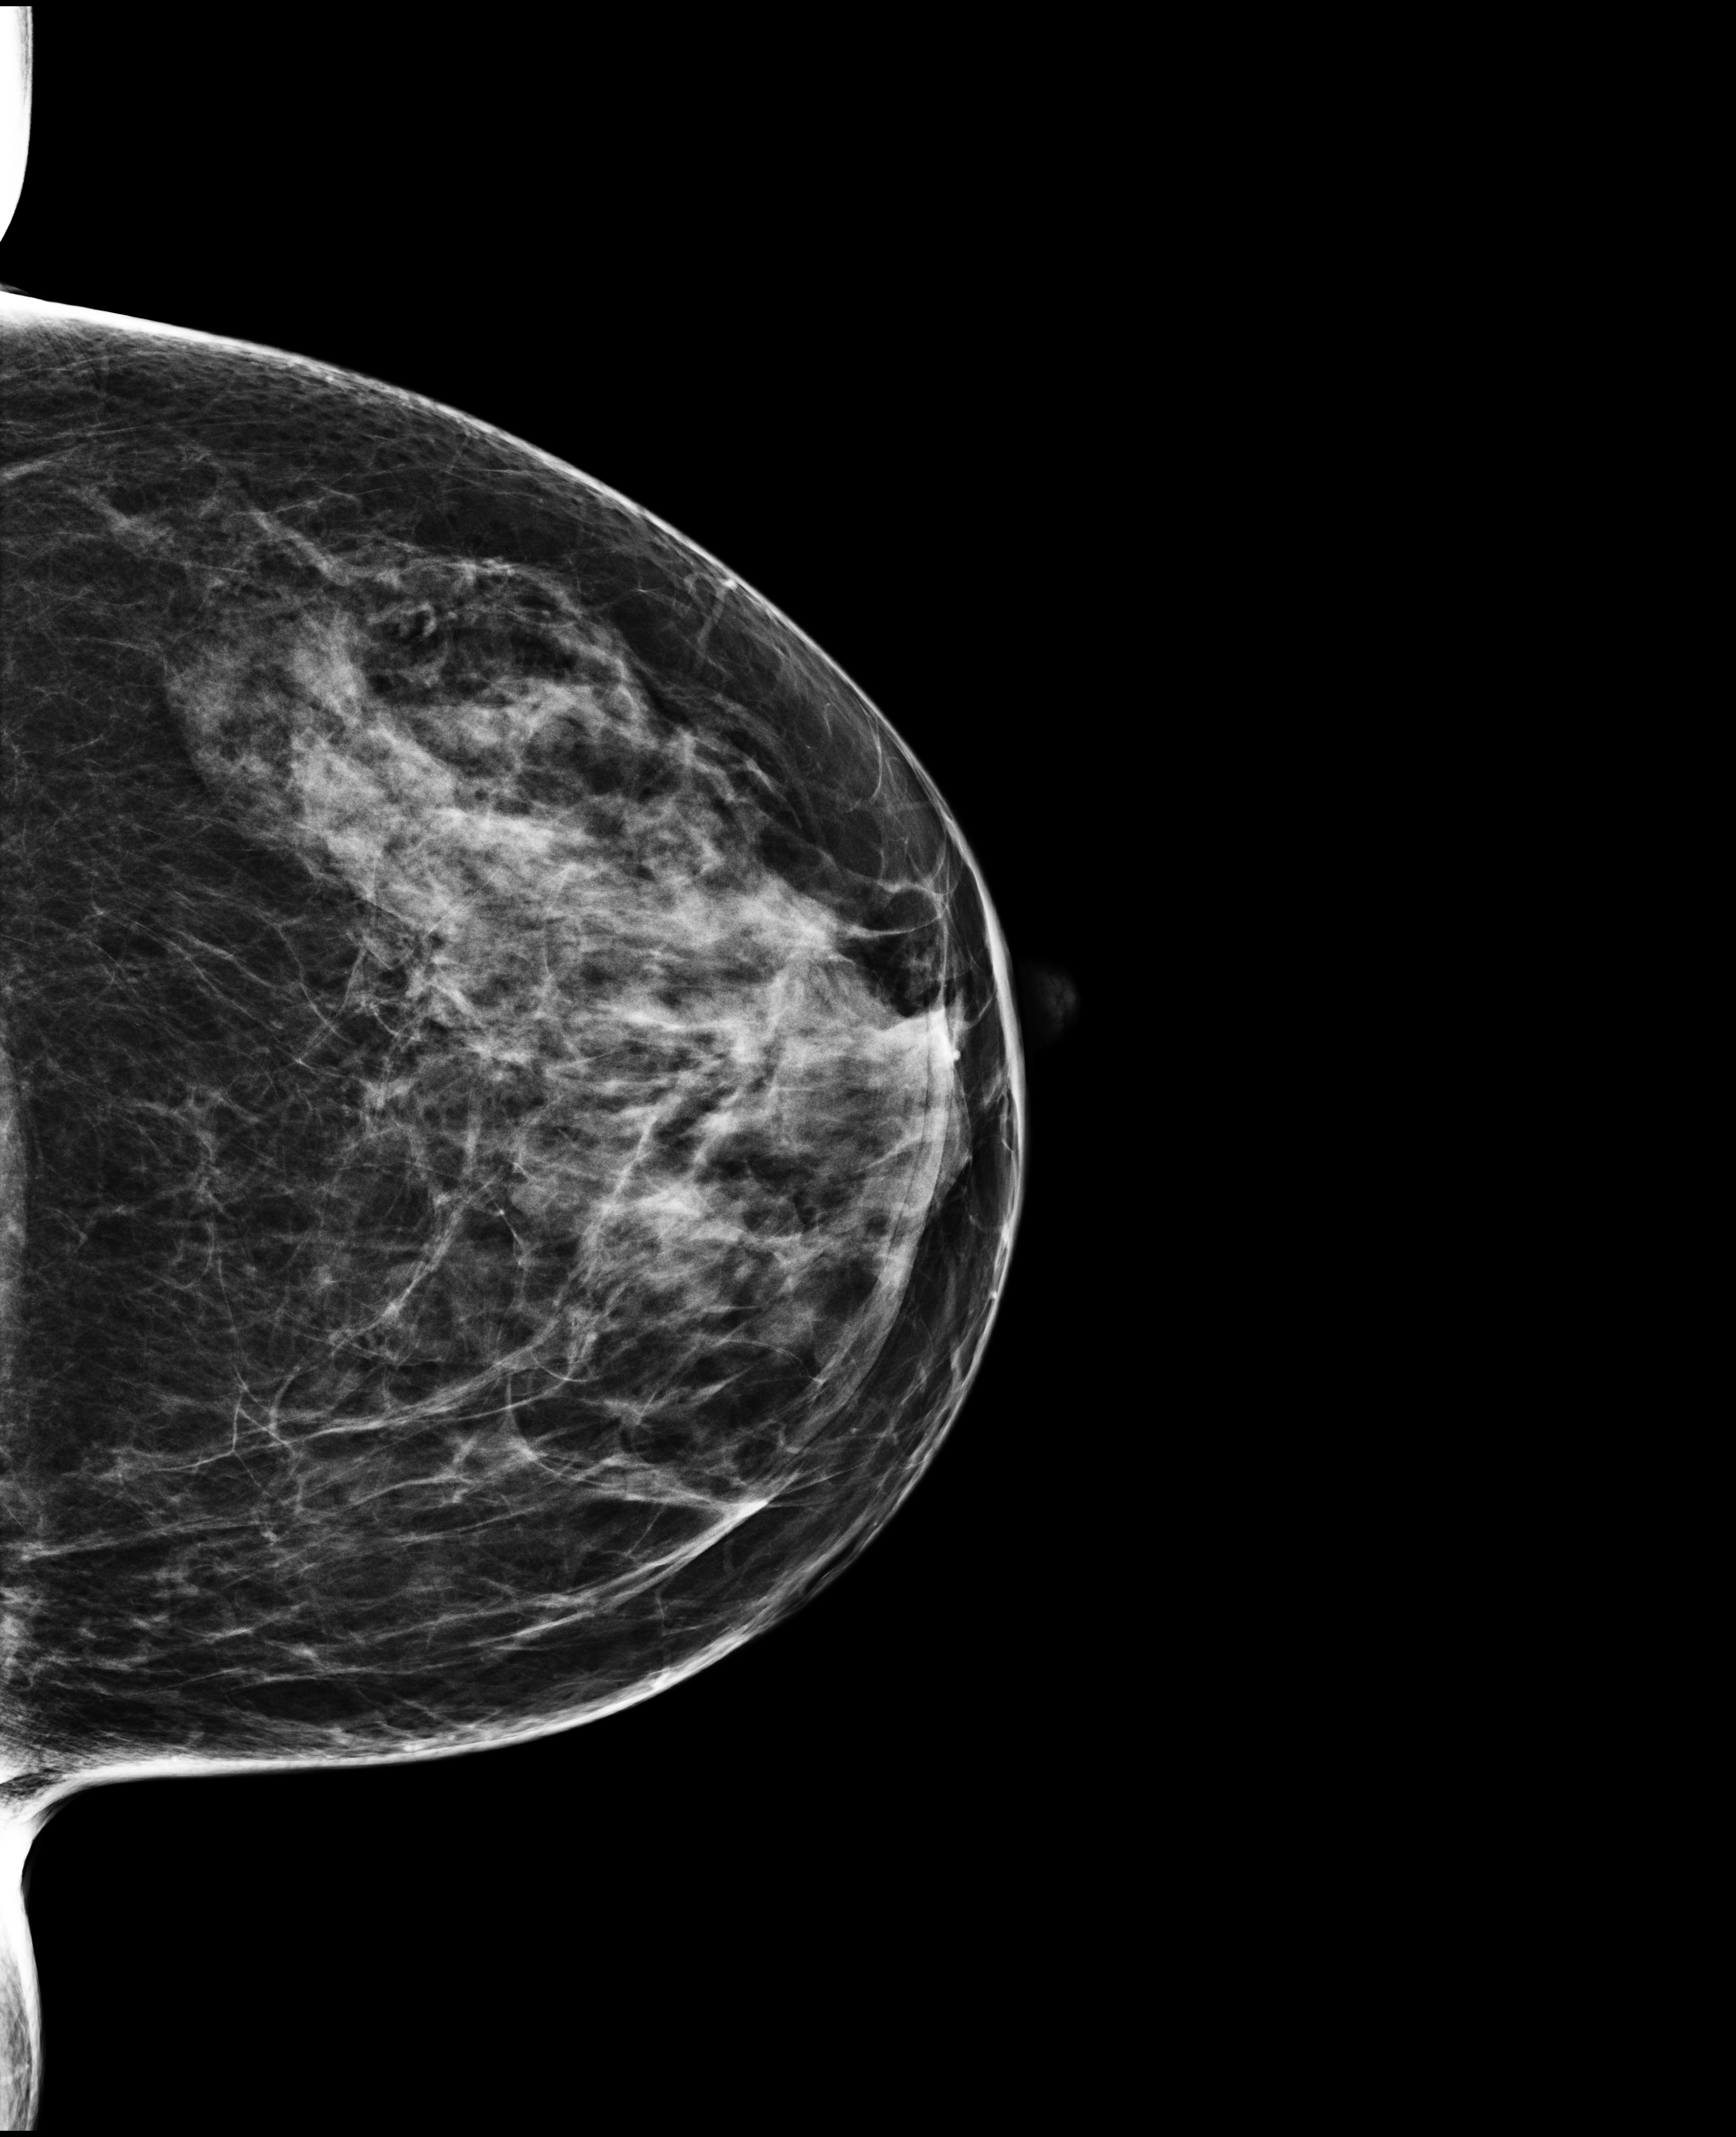
Screening examination. Patient aged 53 years (female).
Image type: full-field digital mammogram. Breast: left. Projection: craniocaudal (CC) view. Breast density at the screening exam (both breasts): scattered fibroglandular densities (BI-RADS density category b). Final BI-RADS category for the screening round (tomosynthesis exam, both breasts): category 1. Recall: no recall after this screen.